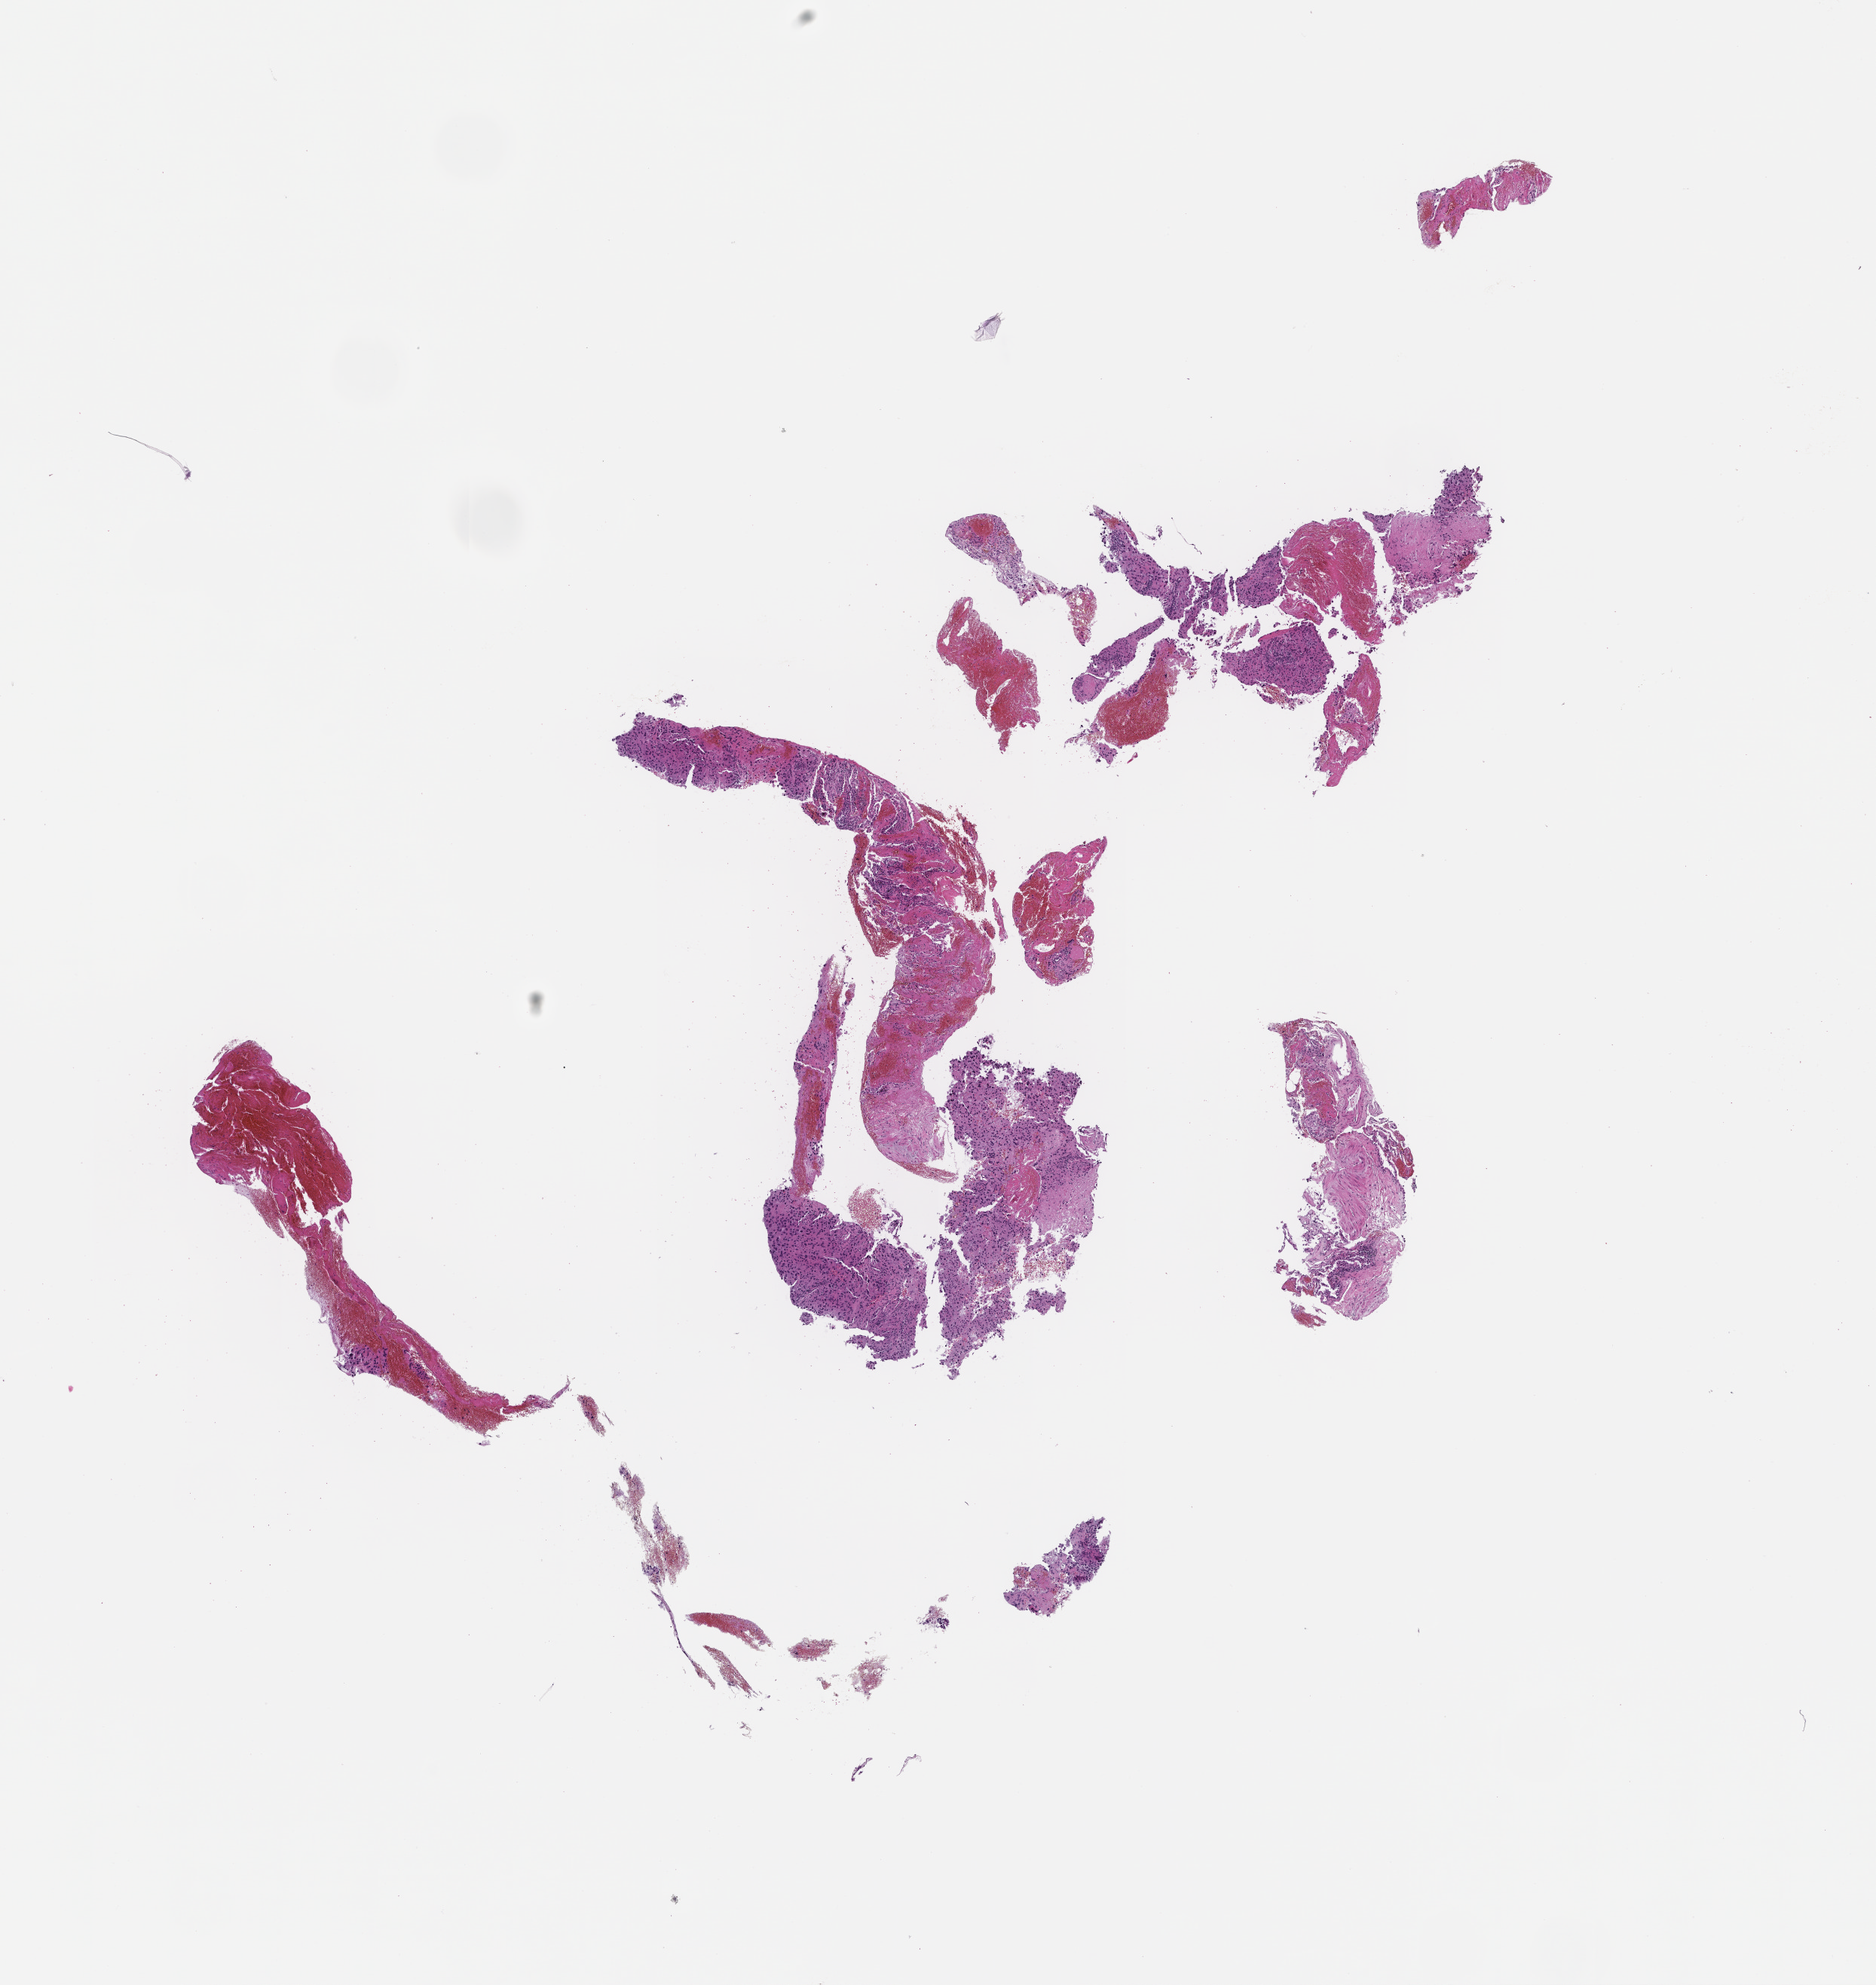
Digitized hematoxylin and eosin (H&E)-stained section — whole scanned area (about 10.1 x 10.6 mm) shown as a low-resolution overview; formalin-fixed paraffin-embedded section; archival tissue. Patient sex: male.
- this section: metastatic tumor tissue
- patient diagnosis (primary): Melanoma